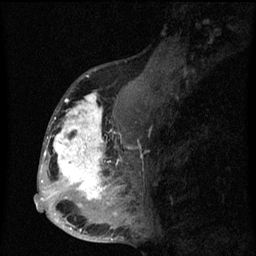
Breast MRI (dynamic contrast-enhanced), one sagittal slice. Position 32 of 60 along the scan axis. Dynamic contrast-enhanced series, image 2 of 3 at this slice position (ordered by acquisition). 1.5 T. TE 4.2 ms, TR 8 ms. 256 × 256 image matrix, field of view 190 × 190 mm. Female patient, age 50 years.
Annotated regions visible in this slice (semi-automatically segmented with operator editing):
- analysis volume of interest (the breast-tissue region the enhancement analysis was run in; not a lesion): bounding box (x1, y1, x2, y2) in pixels: (43, 90, 142, 216)
- tumour enhancement mask (voxels above the 70 % enhancement threshold inside the analysis volume of interest): (43, 93, 122, 204)